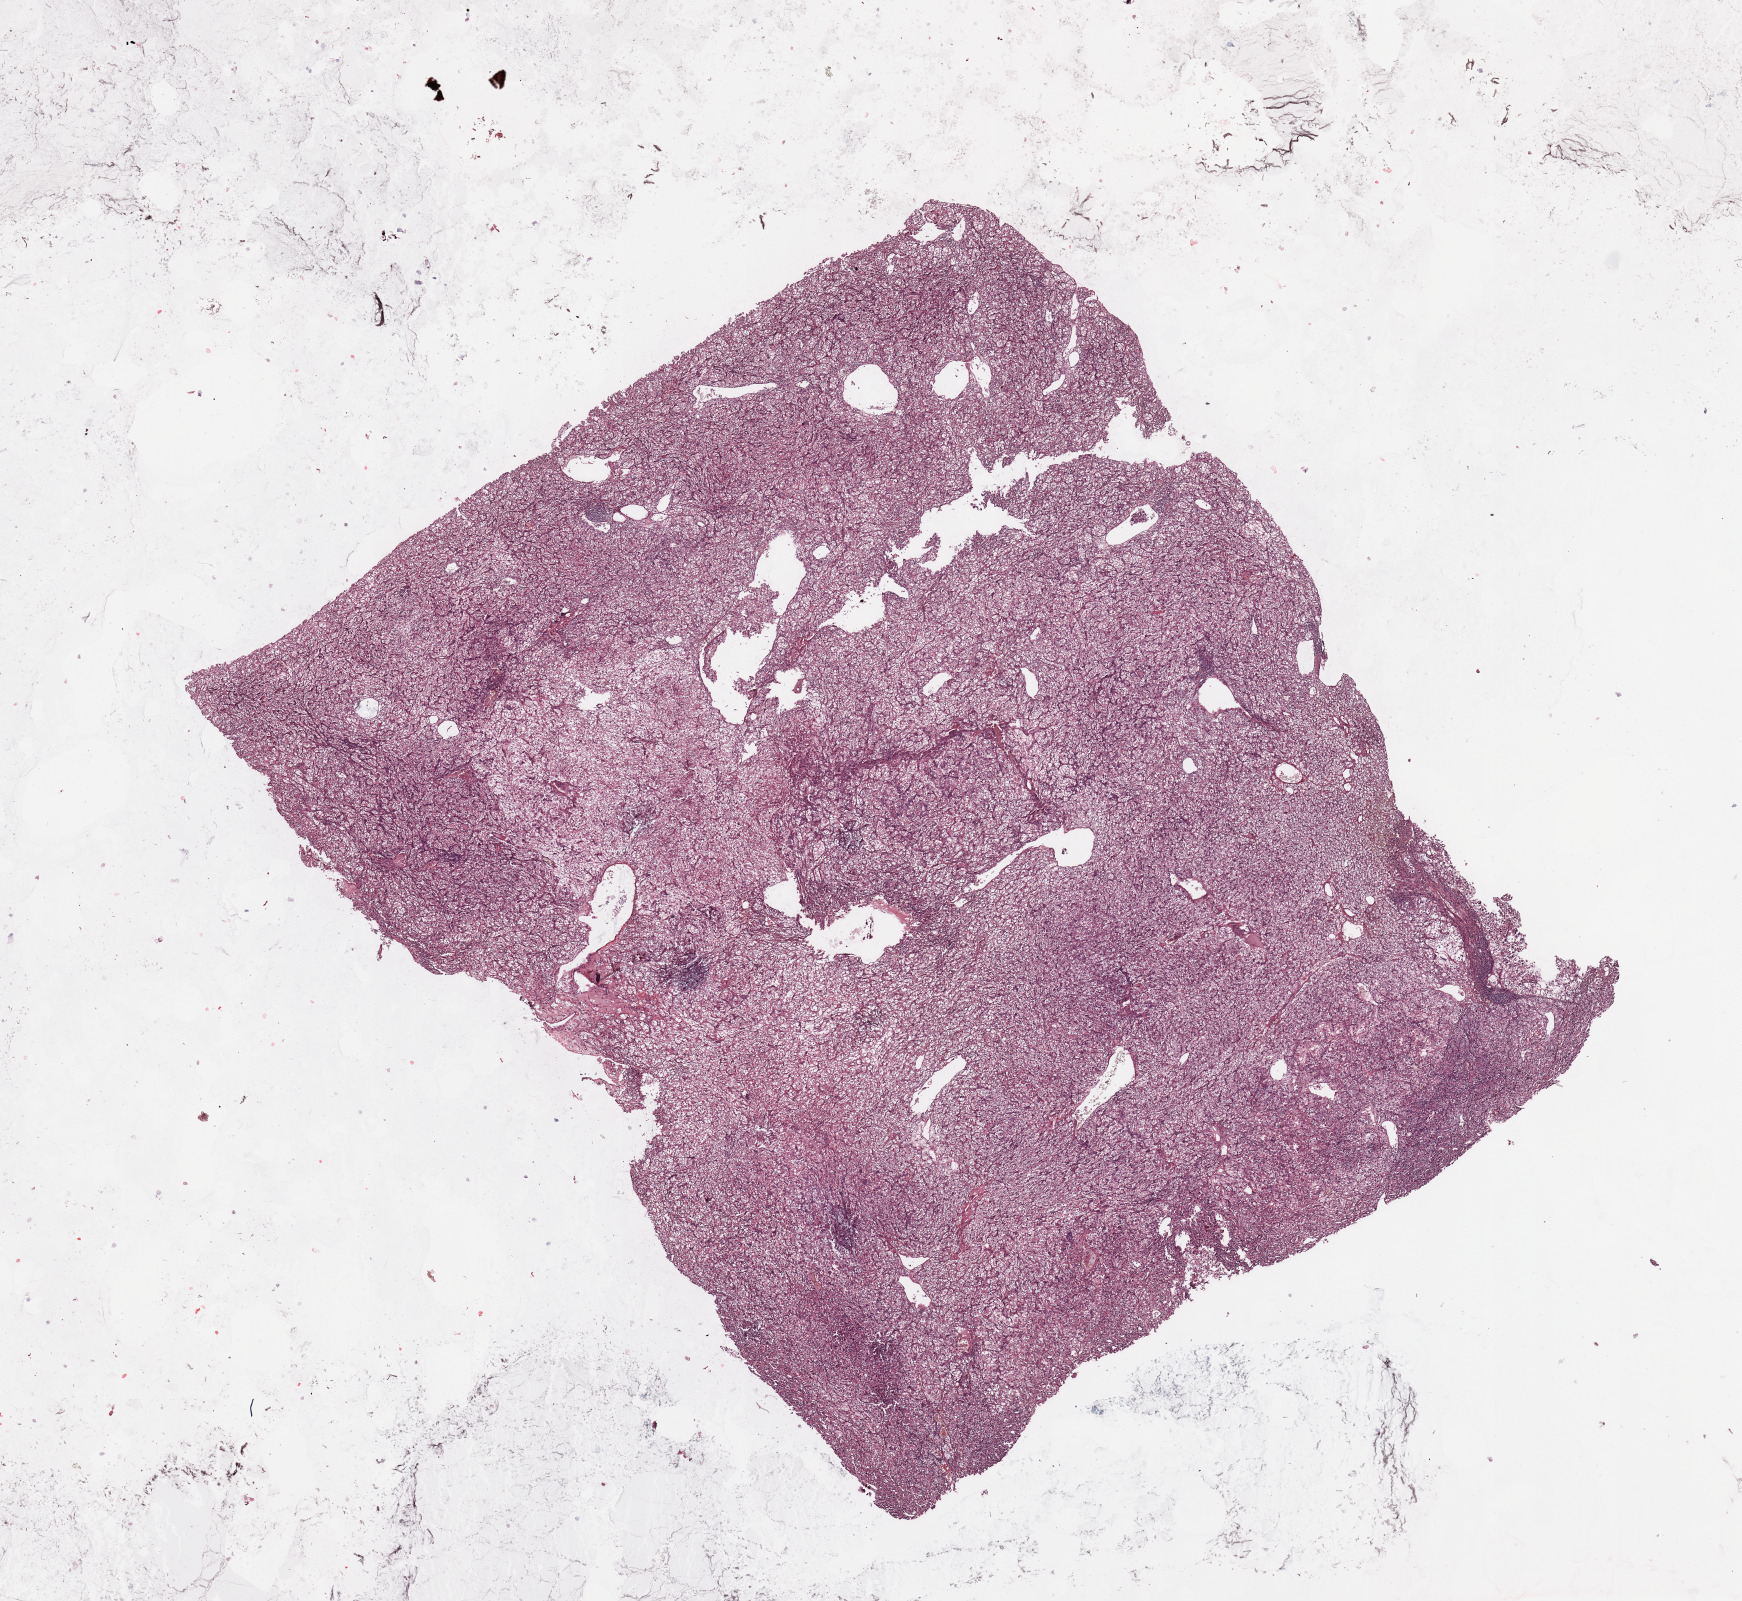
Digitized Hematoxylin and eosin (H&E) stained tissue section (whole slide) — whole scanned area (about 13.8 x 12.7 mm, acquisition: 20x scan) shown as a low-resolution overview; tumour tissue sample, sampled site: kidney. Male, 80 y/o. Histologic grade: G2 (moderately differentiated). Composition of this section per pathologist review: tumour nuclei 90%, necrosis 2%.
• primary tumour site (as recorded): upper pole
• diagnosis: Renal cell carcinoma, NOS
• AJCC pathologic stage: I